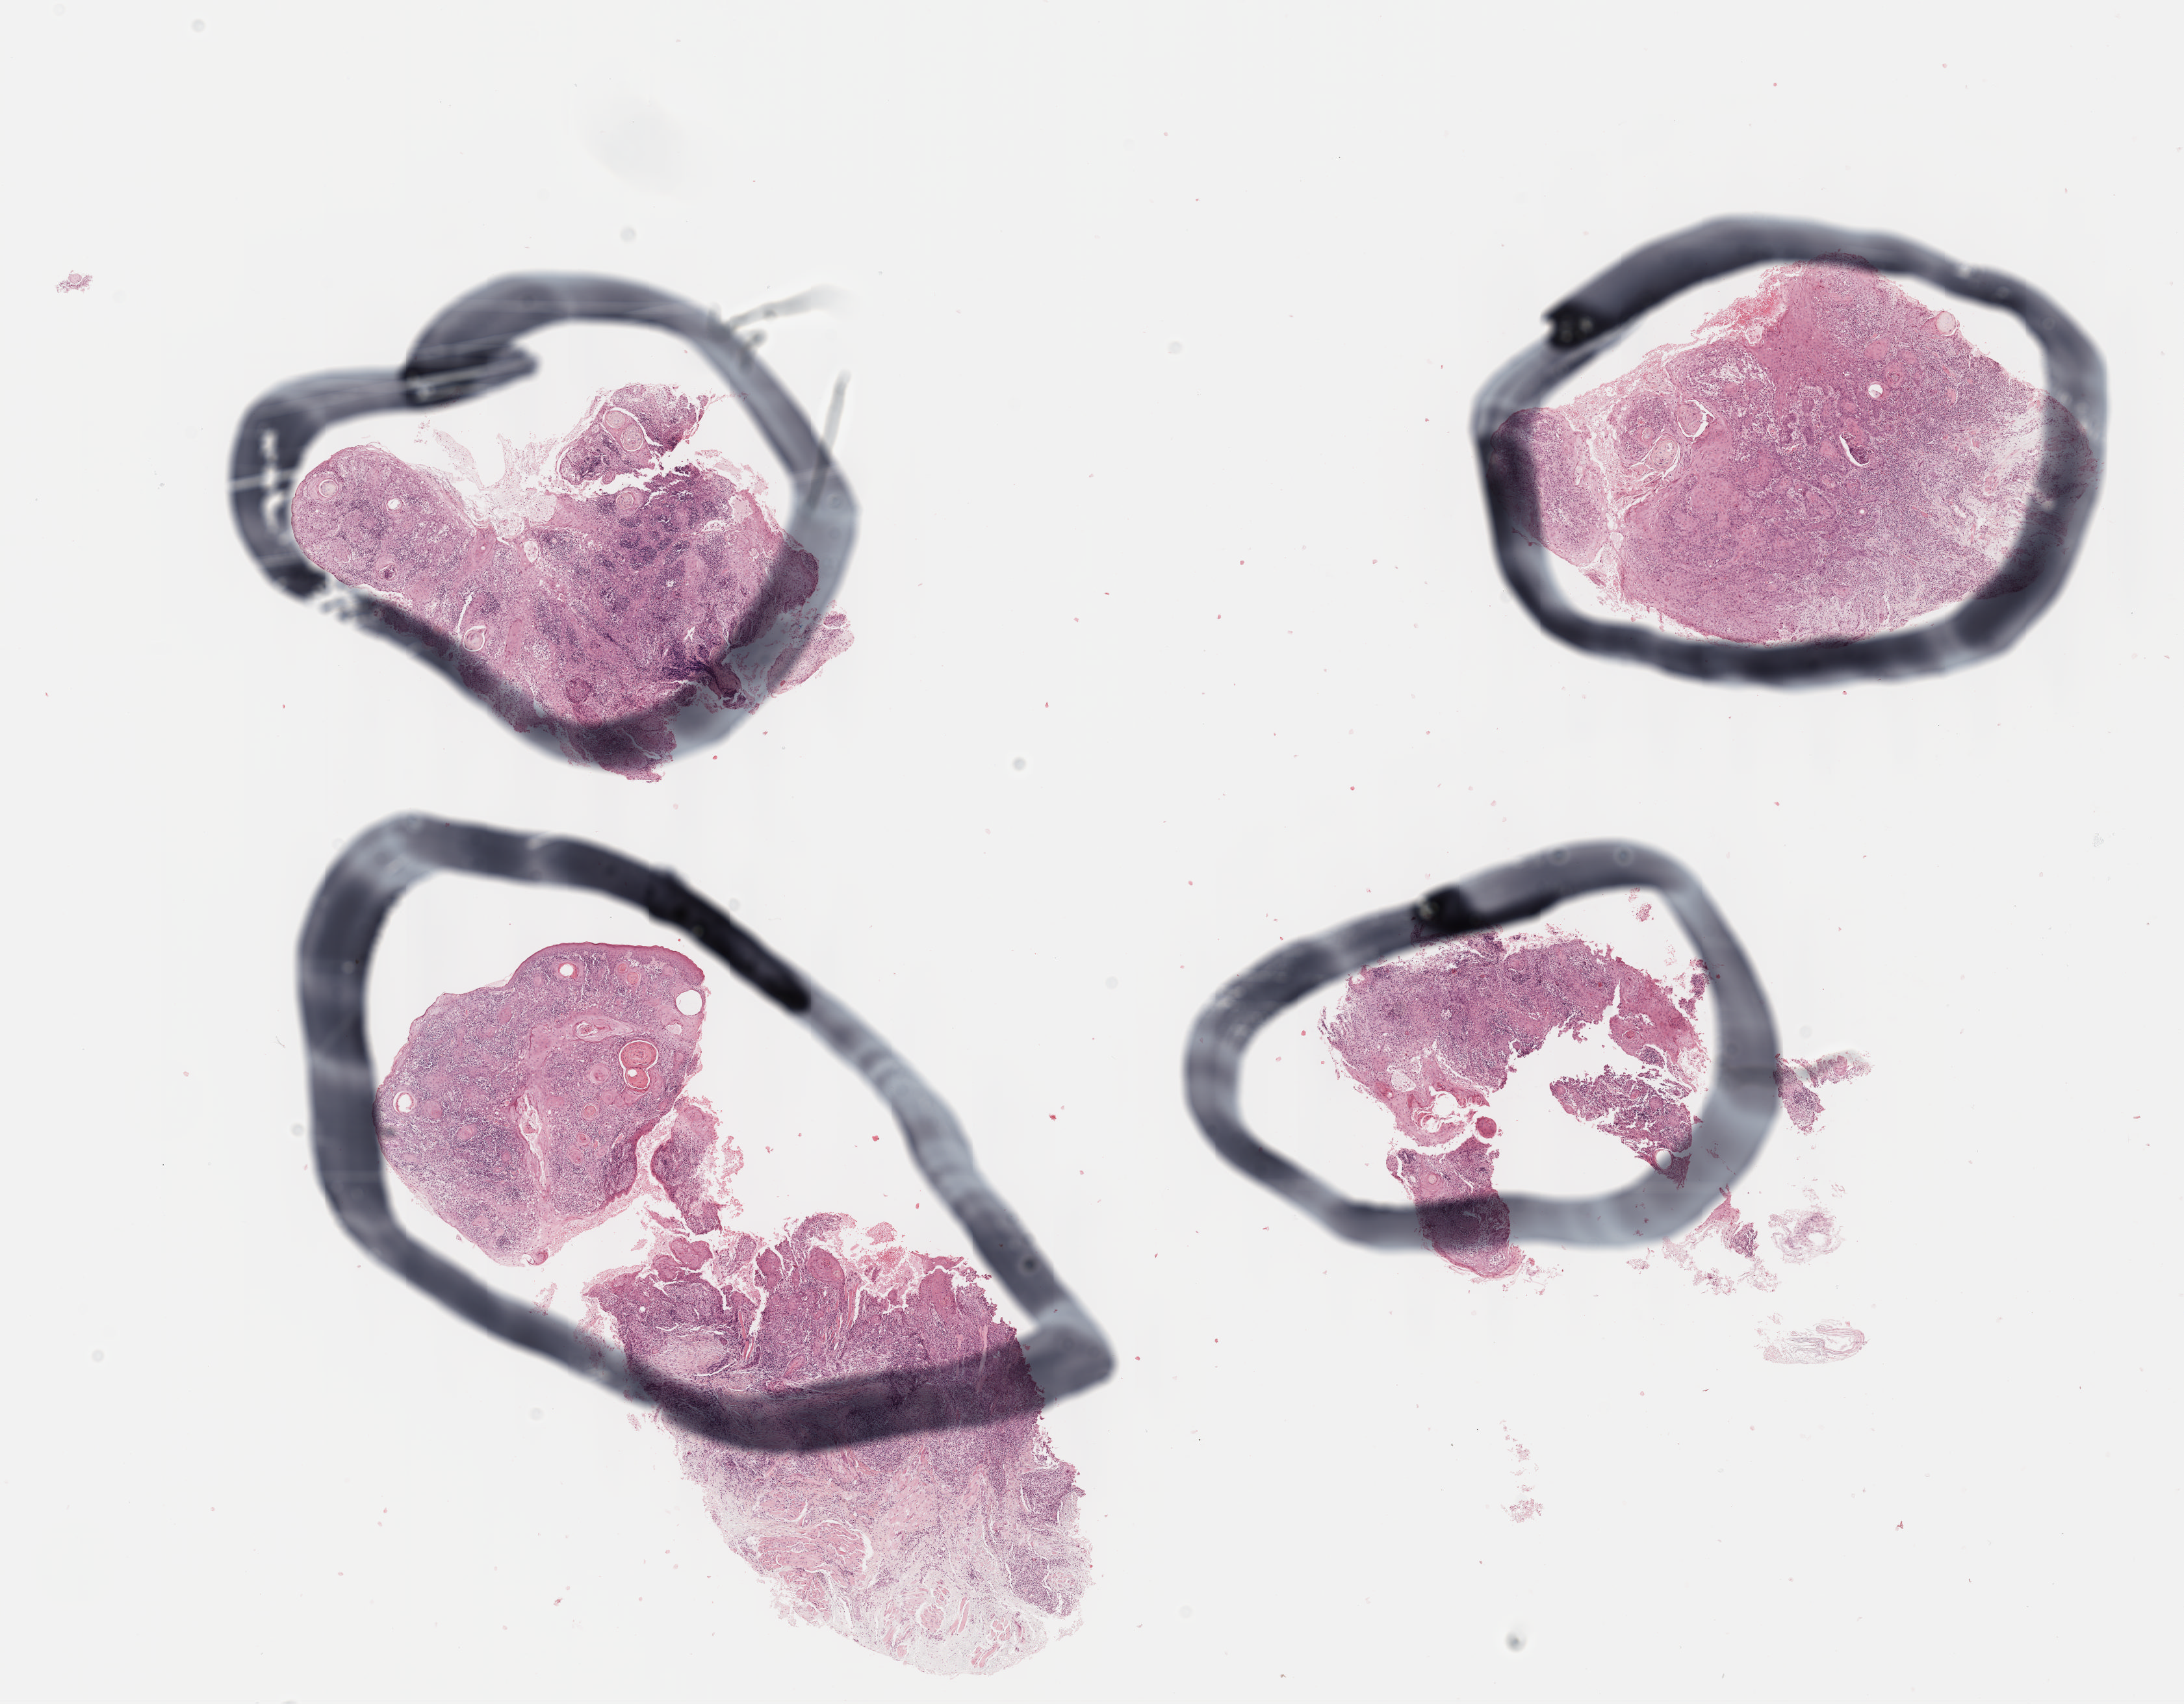
Whole-slide histology image, H&E, a low-resolution overview of the entire scanned area, about 13.6 x 10.6 mm (slide scanned at 40x). FFPE section. Sample: primary tumour, head and neck. Male patient; age at initial diagnosis 57 years. Histologic grade: G2 (moderately differentiated).
* lymph nodes positive (case pathology): 3 of 42 examined
* pathologic diagnosis: Squamous cell carcinoma, NOS (tongue, NOS)
* laterality: left